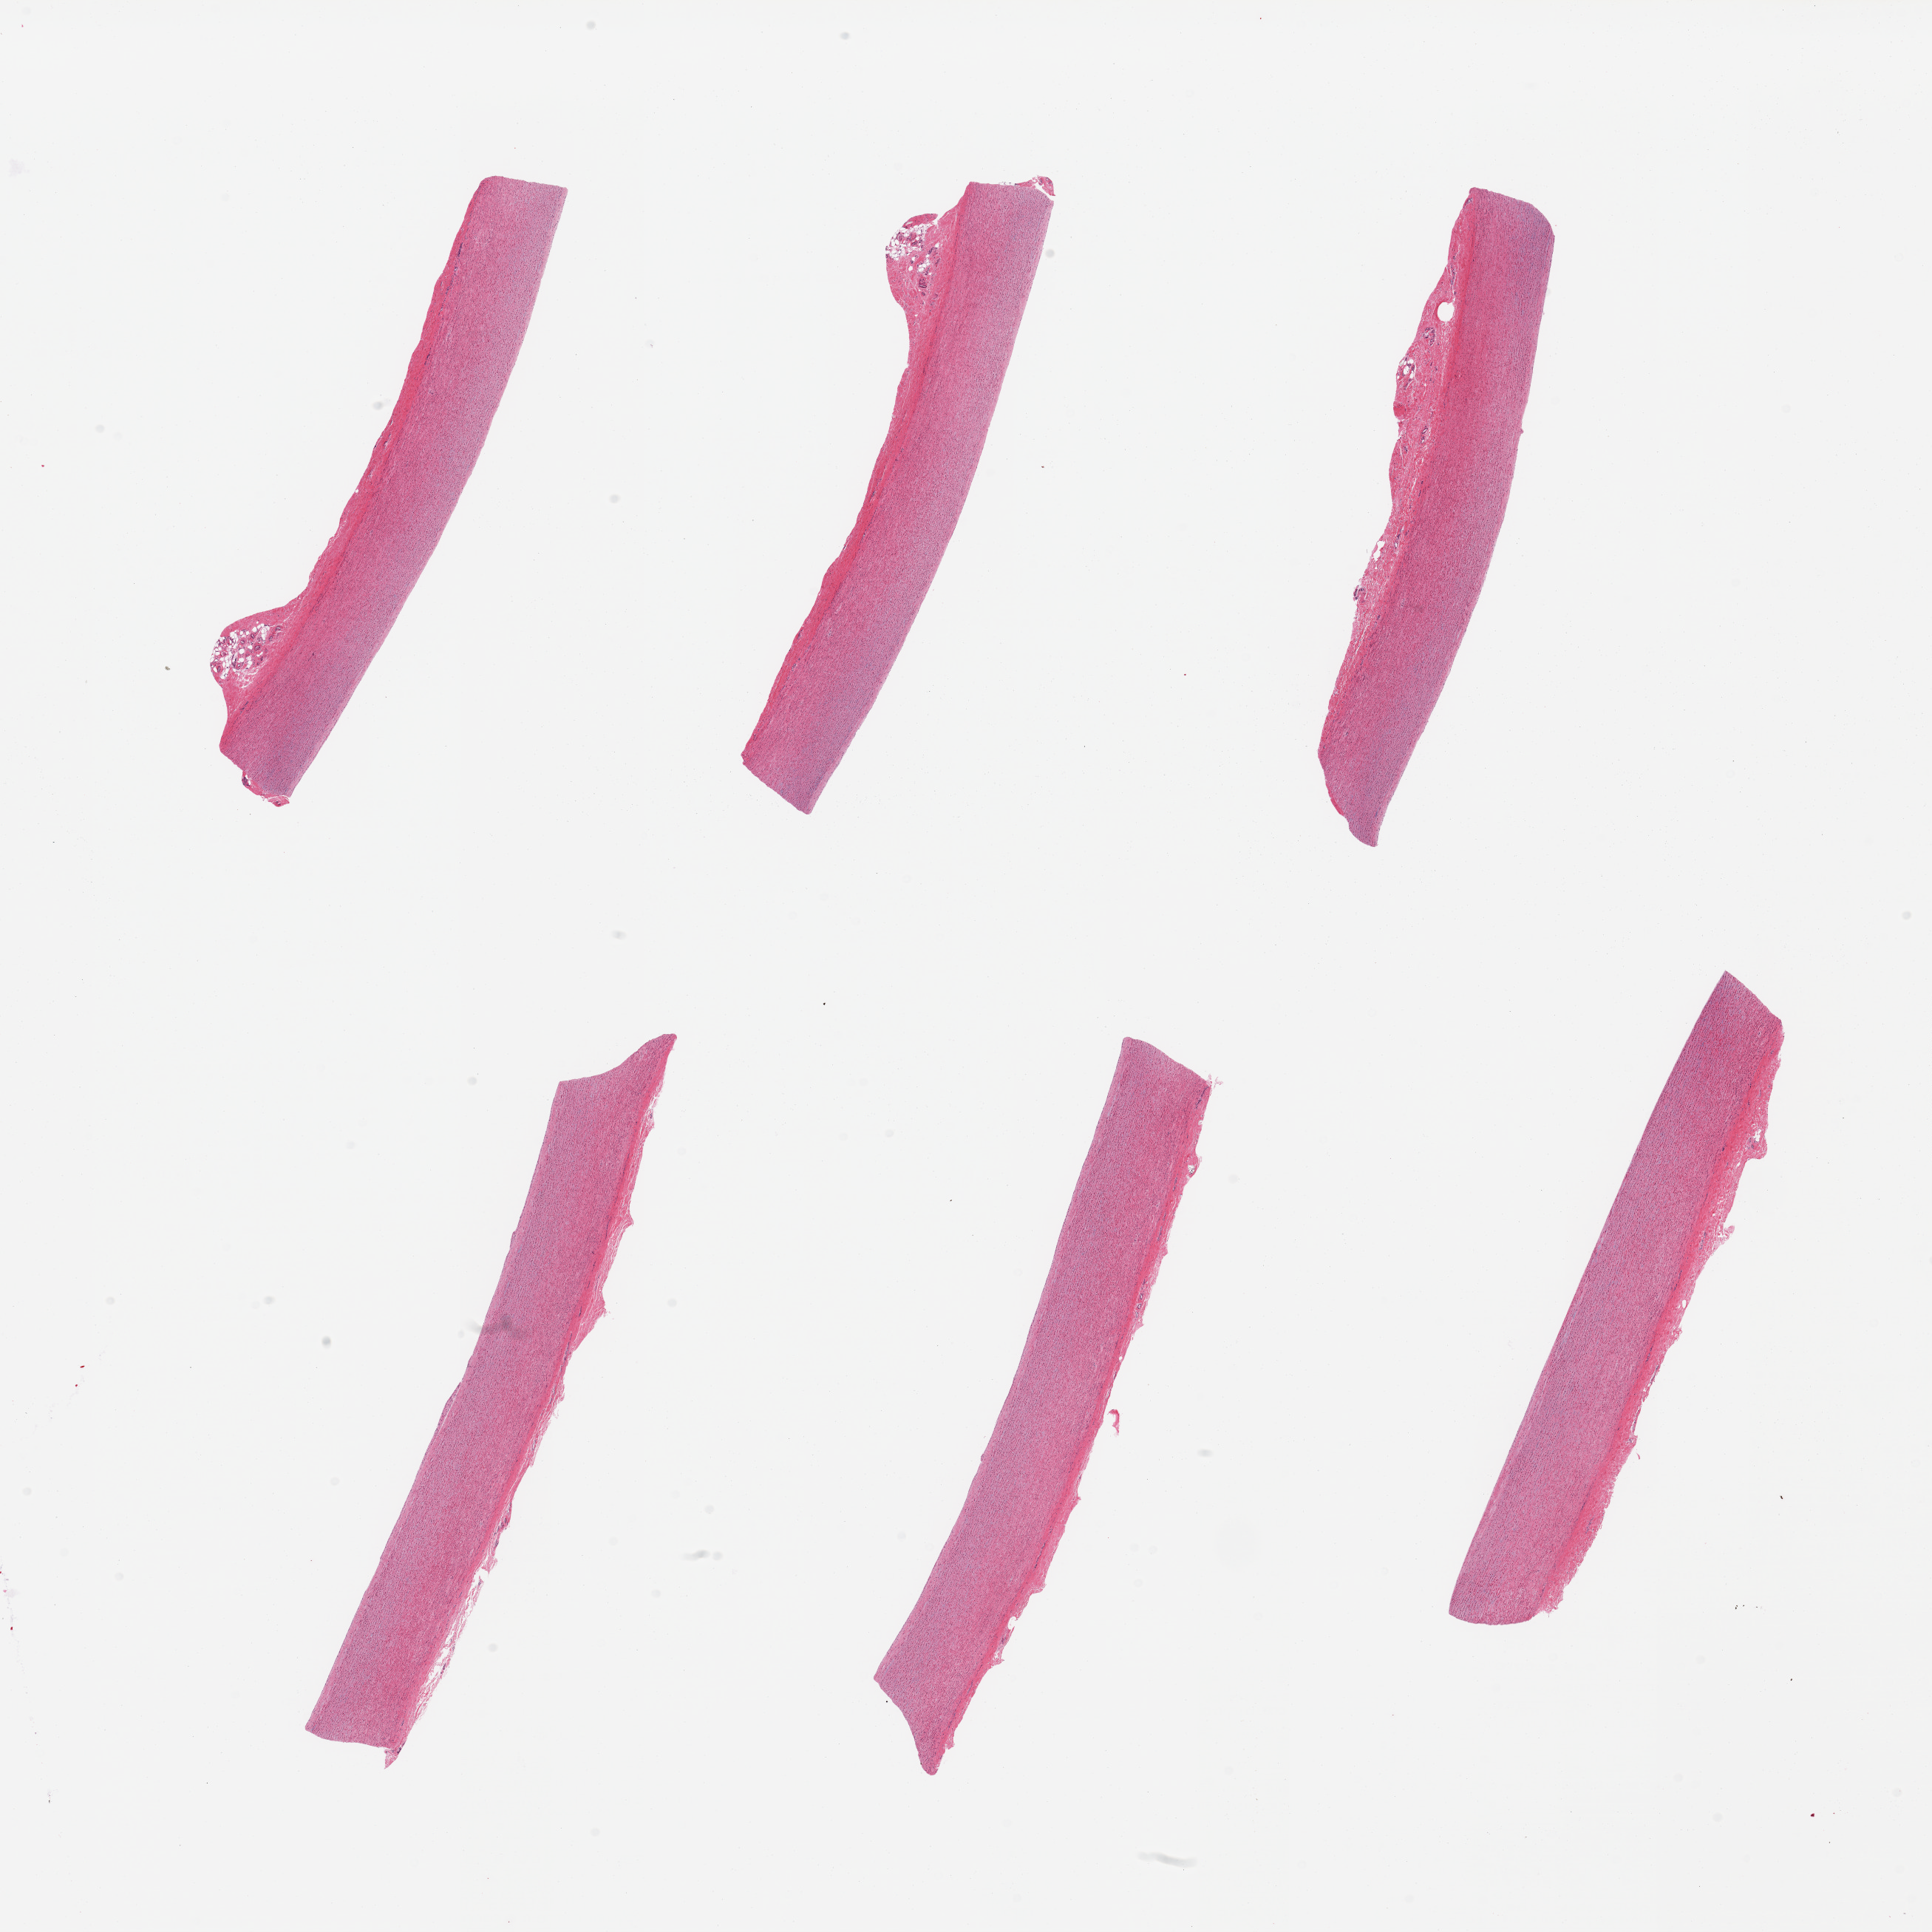
Hematoxylin and eosin (H&E) whole-slide image — low-resolution overview of the scanned area, about 20.7 x 20.7 mm; PAXgene-fixed, paraffin-embedded tissue; section of aorta (target tissue); donor tissue sample. Donor sex: female.
Reviewer comment on this tissue sample: 6 pieces; up to ~0.7mm attached adventitia.